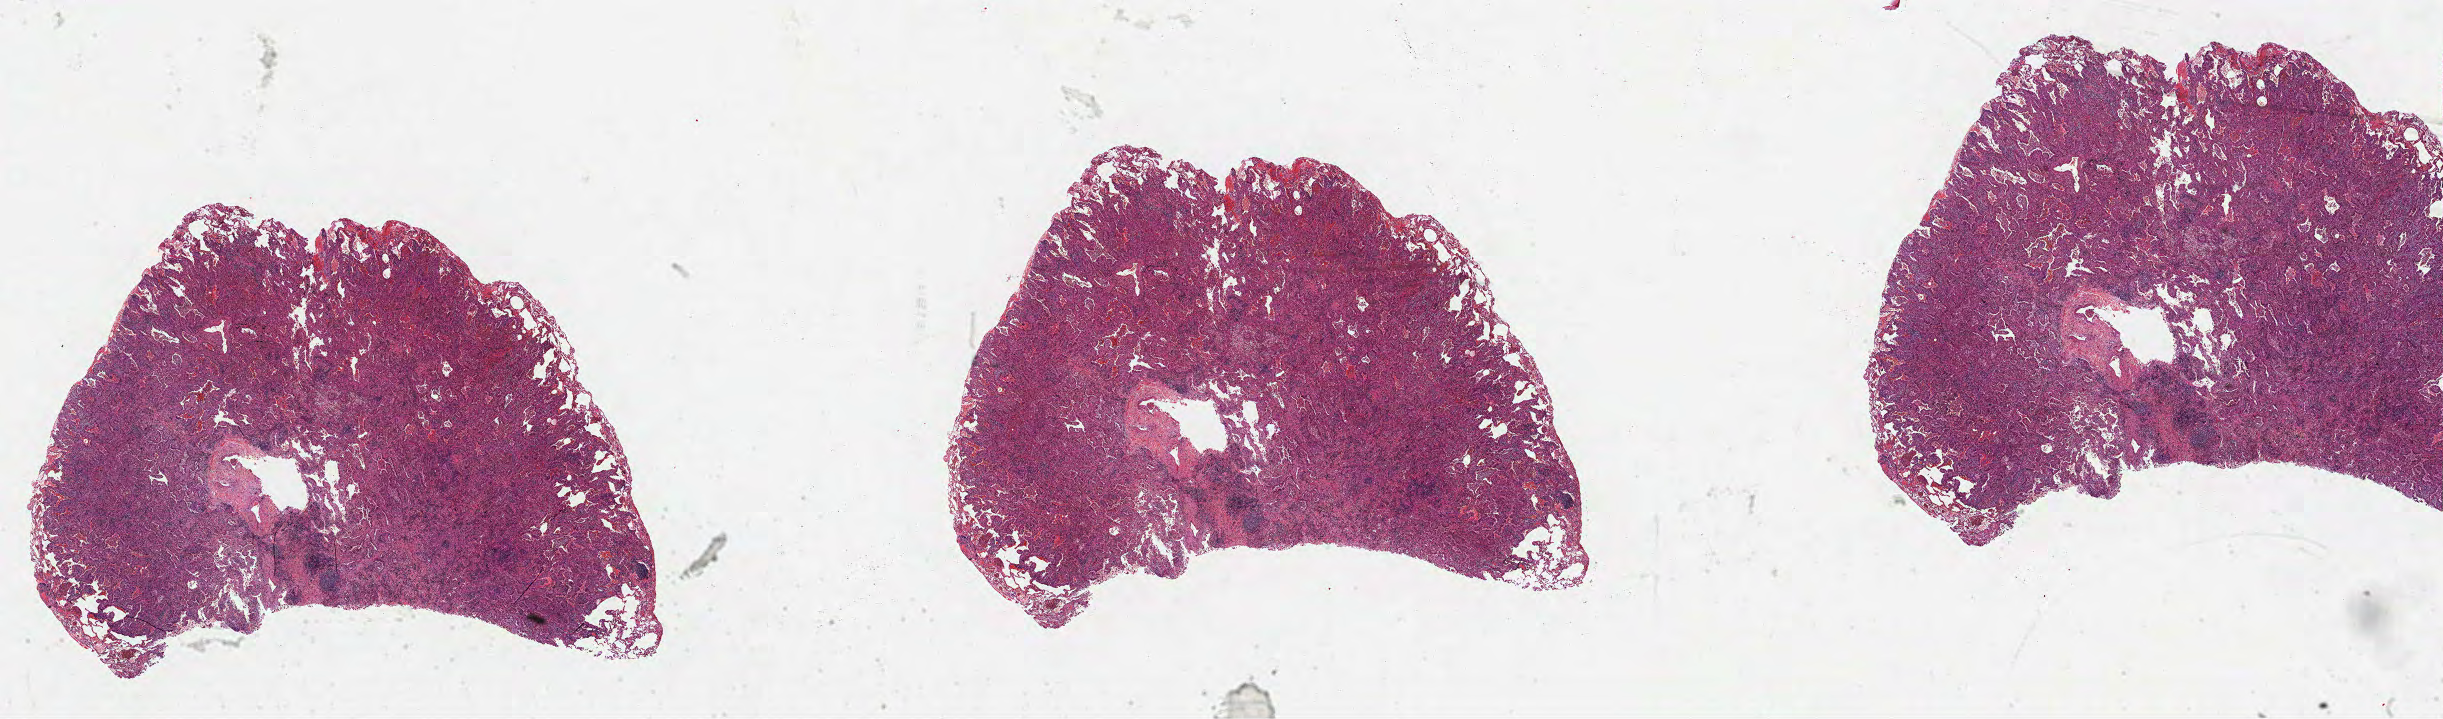
H&E-stained whole-slide image — whole scanned area (about 39.4 x 11.6 mm, slide scanned at 40x) shown as a low-resolution overview, FFPE section, primary tumour sample from the lung. Patient: female, age at initial diagnosis 69 years.
- pathologic diagnosis: Adenocarcinoma, NOS (upper lobe, lung)
- laterality: left
- AJCC pathologic stage: IA